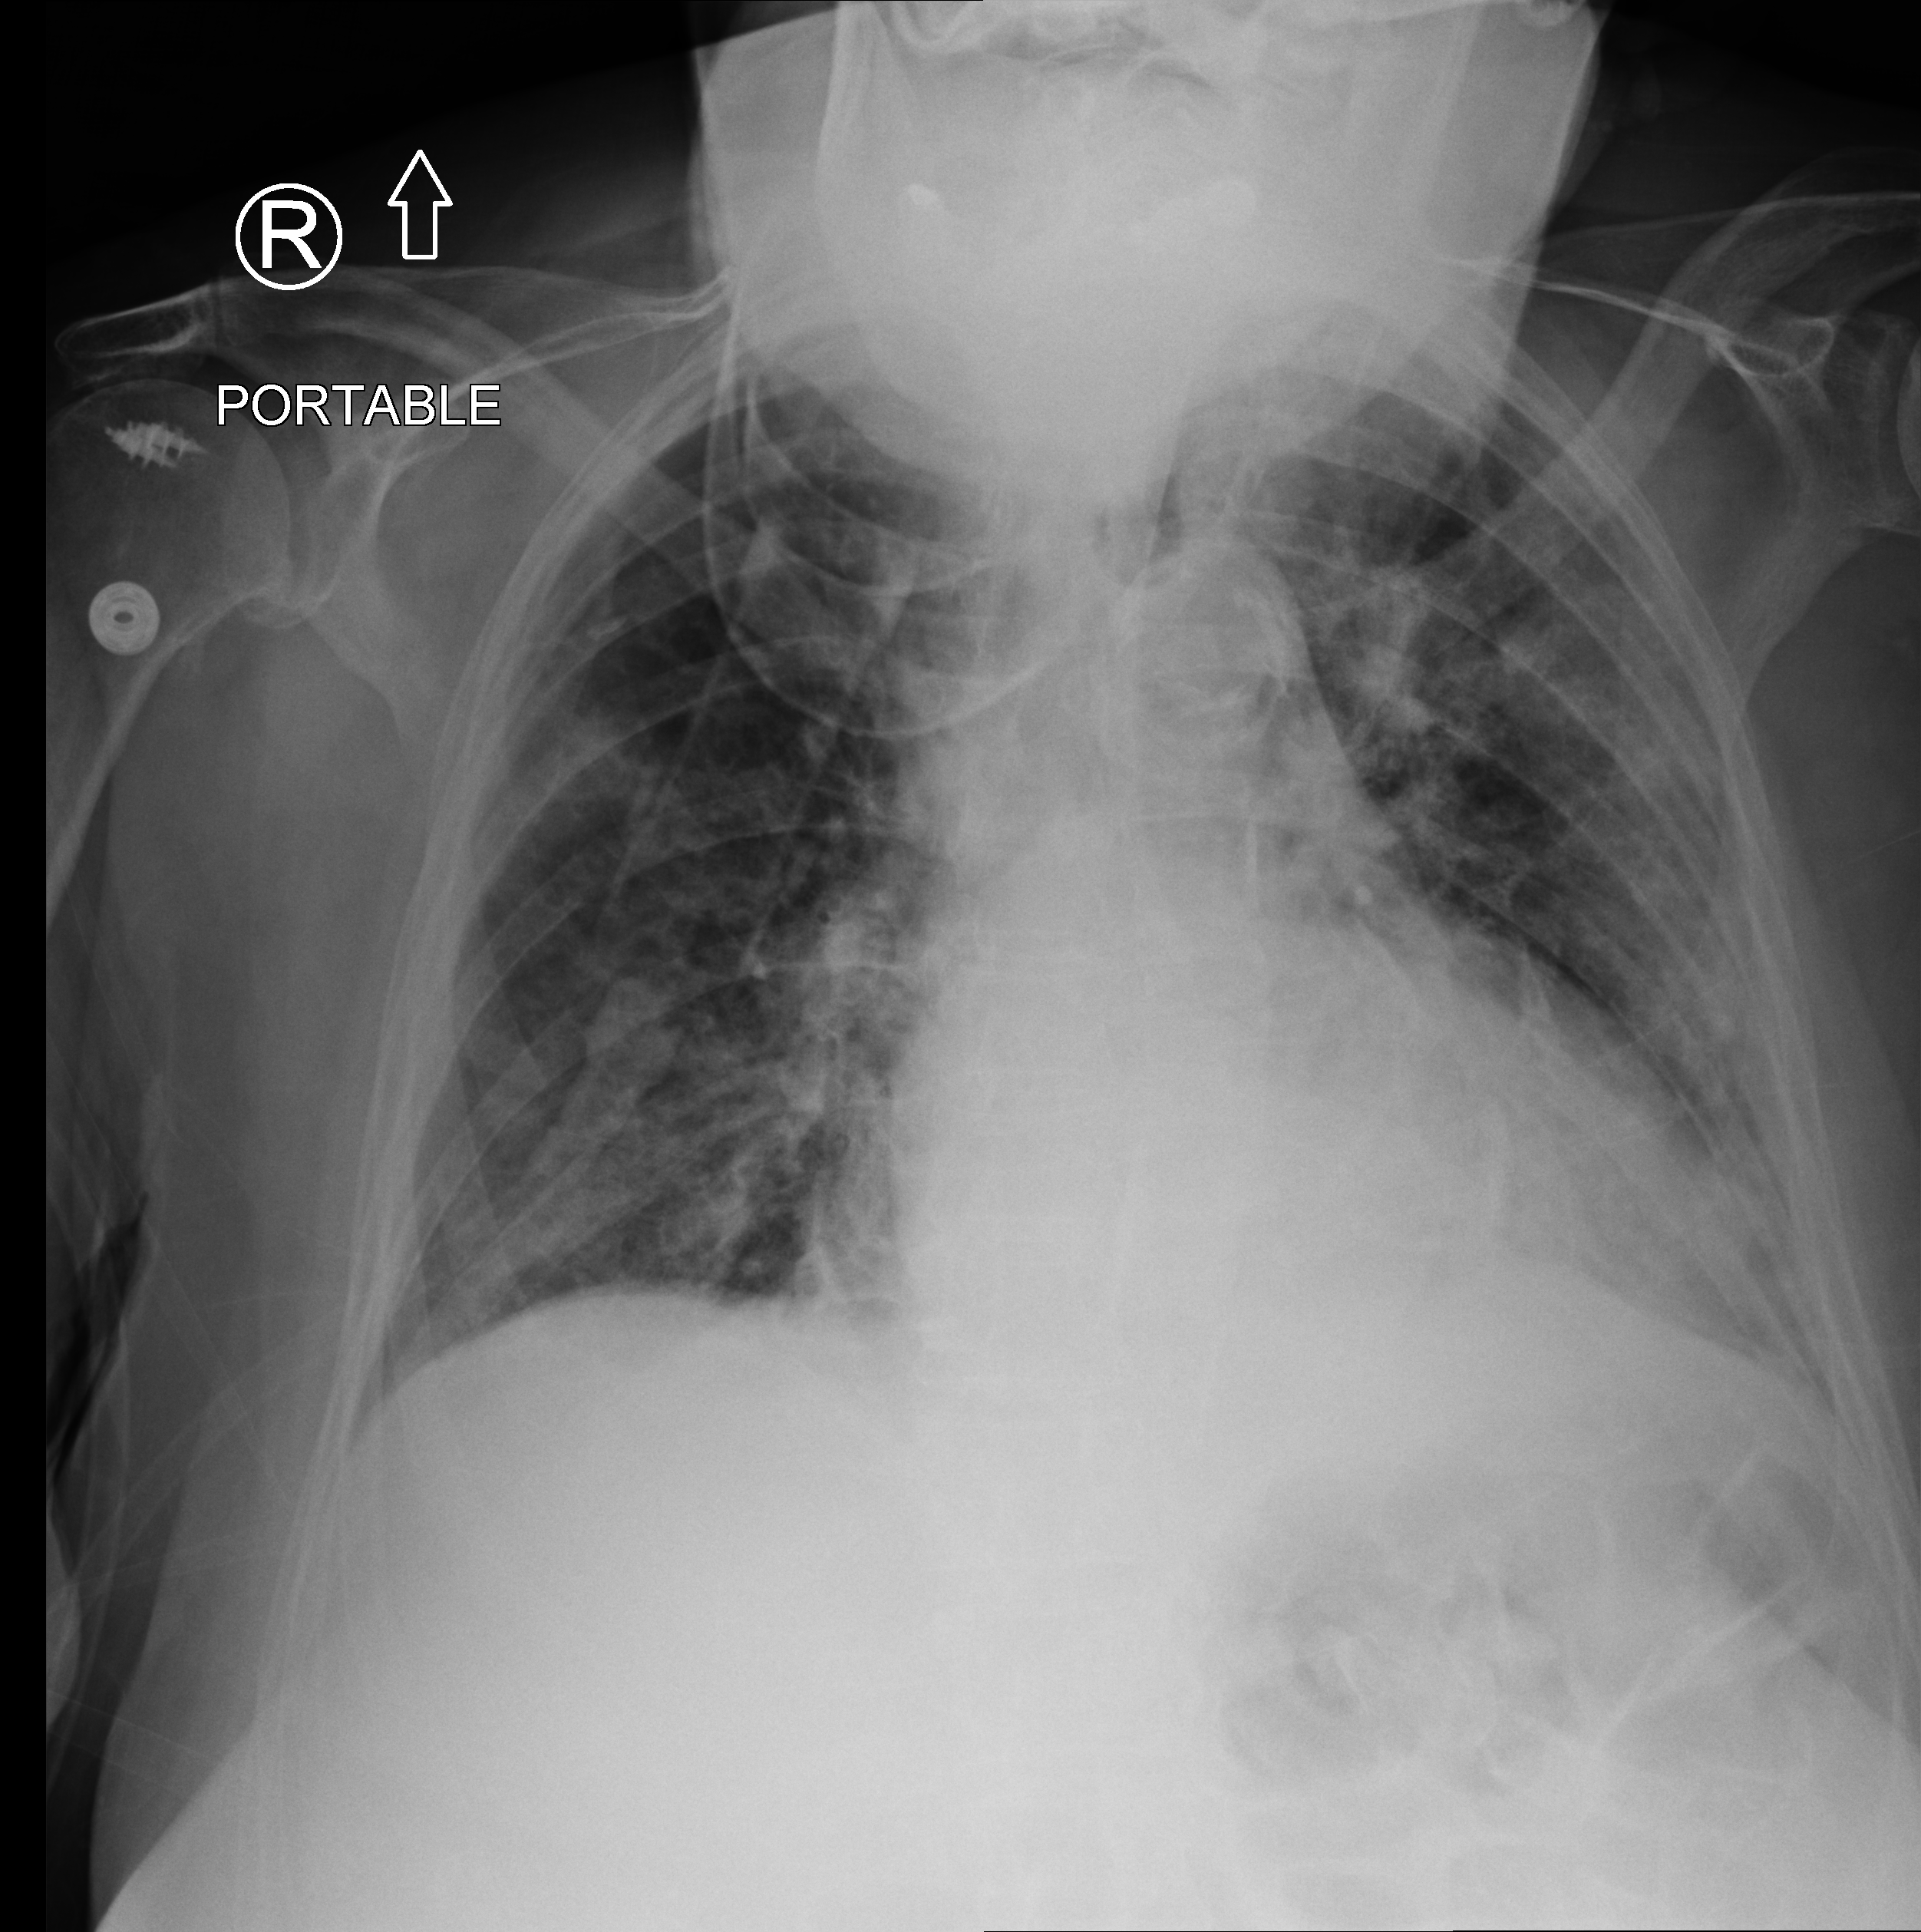
Portable chest radiograph. Patient hospitalised with COVID-19; female, aged 75–90 years.
From the hospital-stay record, not from the radiograph (when in the stay this image was taken is not recorded): admitted to intensive care during this hospital stay: no; length of hospital stay: 13 days; mechanically ventilated during this hospital stay: no.